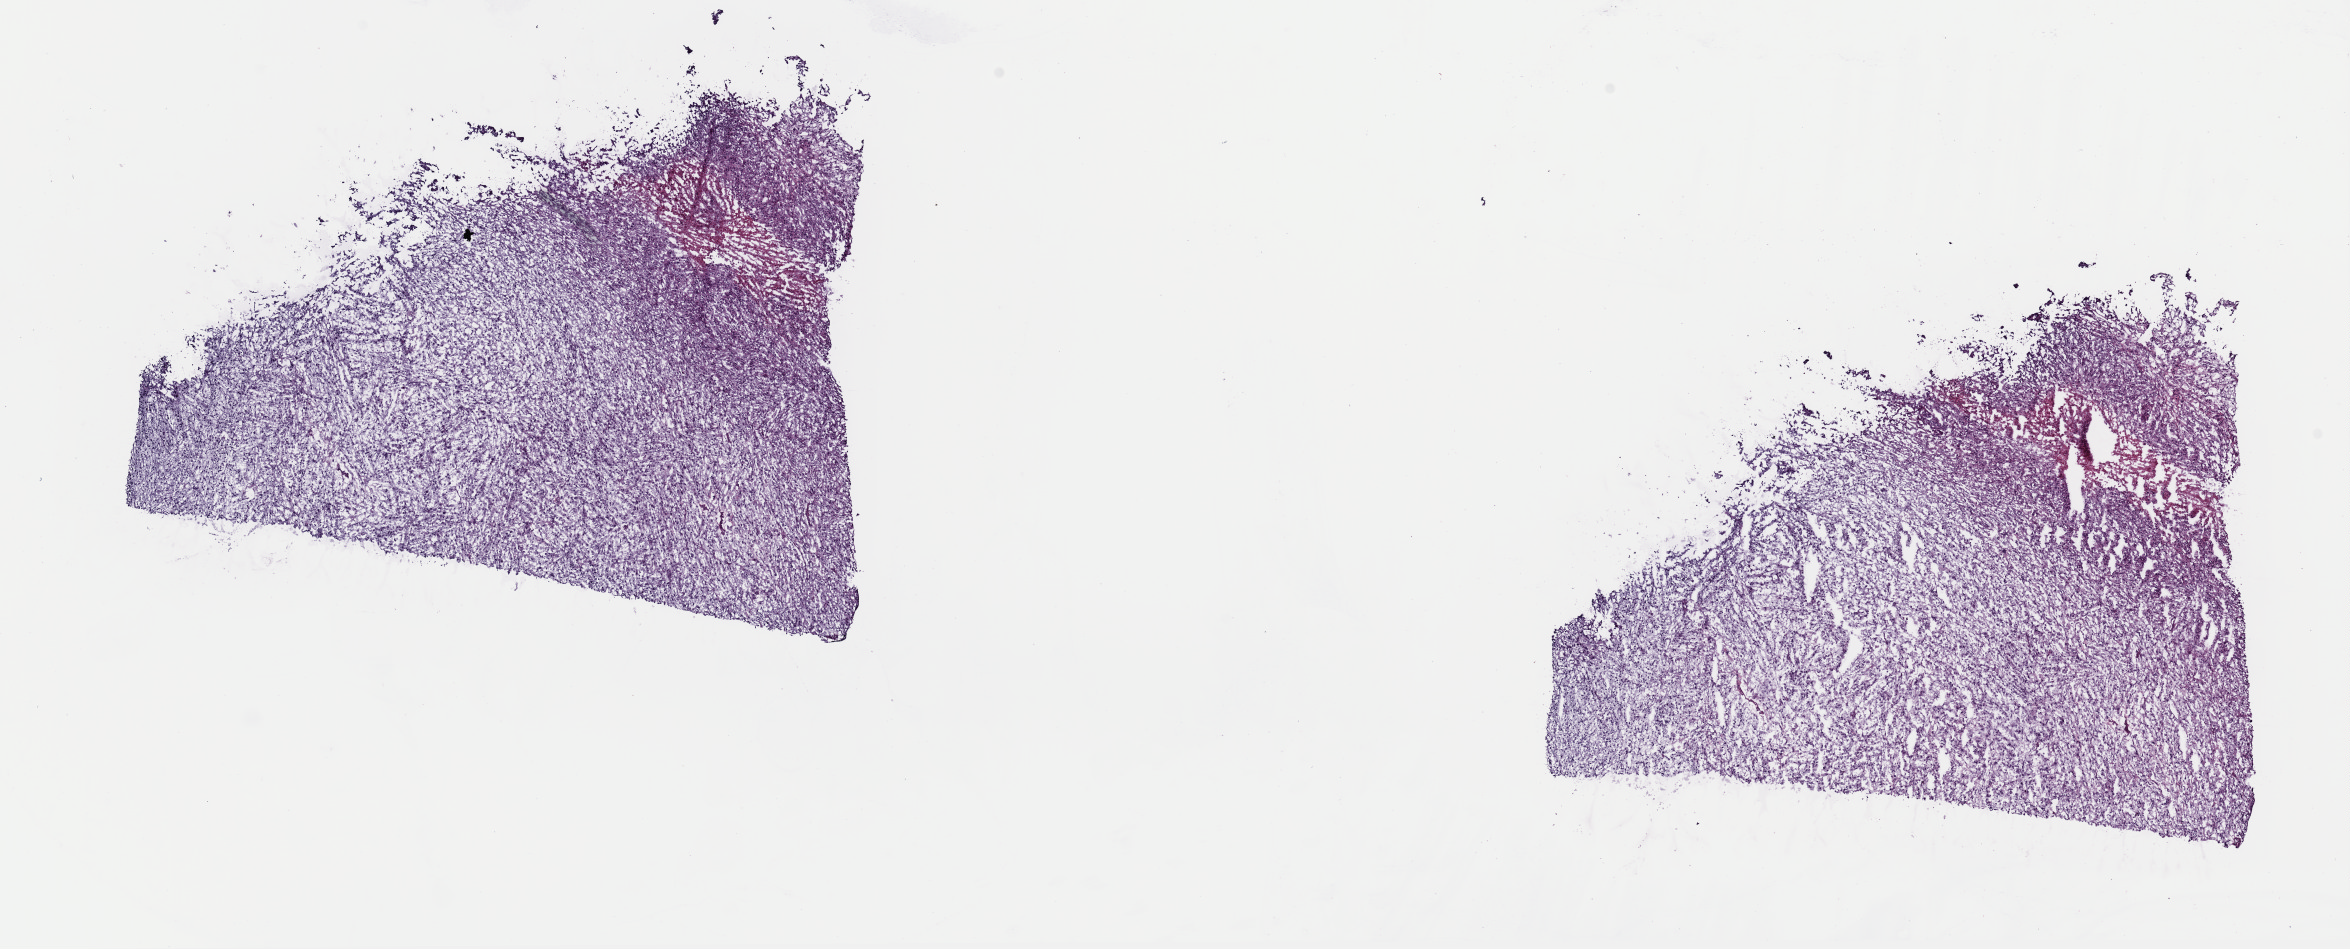
Digitized H&E tissue section (whole slide) — whole scanned area (about 18.6 x 7.5 mm, acquisition: 40x scan) shown as a low-resolution overview. Frozen section from the top of the tissue portion. Primary tumour sample from the uterus. Patient: female, age at initial diagnosis 55 years. Composition of this section per pathologist review: tumour cells 90%, tumour nuclei 90%, normal cells 0%, stromal cells 5%, necrosis 5%. Infiltration values recorded for this section: lymphocyte infiltration 40%, monocyte infiltration 20%, neutrophil infiltration 20%.
Diagnosis: Mullerian mixed tumor (endometrium). FIGO stage: IB.